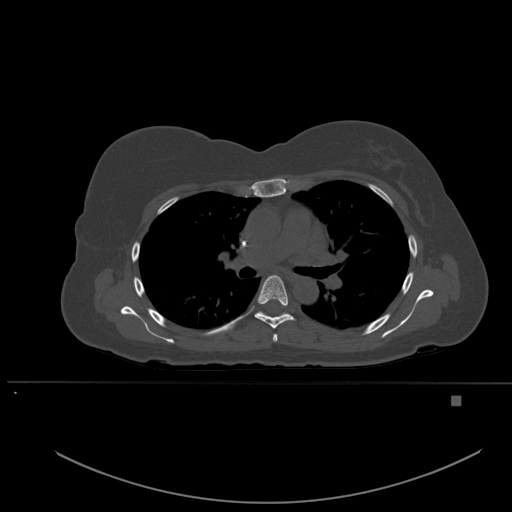
CT including the spine, one axial slice. Slice 364 of 651 in the series (ordered by position). Bone window (W 1800 / L 400 HU). 1.5 mm slice thickness. 512 × 512 image matrix, field of view 443 × 443 mm. Patient: female, 49 years. Case-level facts recorded for this patient, not image findings: primary cancer: breast.
Structures marked on this image (semi-automatic segmentation, software-assisted and operator-edited):
- T4 vertebra: bounding box [x1, y1, x2, y2] px = [273, 334, 278, 342]
- T5 vertebra: [255, 275, 295, 329]
- T6 vertebra: [258, 312, 284, 316]